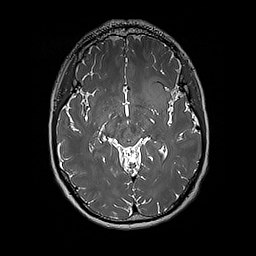
Brain MRI from a brain-tumour surgery series, one axial slice. Slice 108 of 192 in the series (ordered by position). 1 mm slice thickness. 256 × 256 image matrix, field of view 250 × 250 mm. From the clinical record (not read from this slice): histopathology: Glioblastoma; WHO grade: 4; IDH mutation: no.
Outlined on this slice (manually delineated by an expert):
- tumour: bounding box [x1, y1, x2, y2] px = [142, 76, 170, 109]